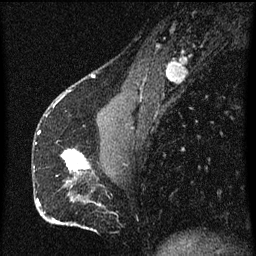
Breast MRI (dynamic contrast-enhanced), one sagittal slice; position 24 of 60 along the scan axis; dynamic contrast-enhanced series, image 2 of 3 at this slice position (ordered by acquisition); 1.5 T; TE 4.2 ms, TR 8 ms; 2 mm slice thickness; 256 × 256 image matrix, field of view 180 × 180 mm. Patient: female, 51 years.
Structures marked on this image (semi-automatically segmented with operator editing):
- analysis volume of interest (the breast-tissue region the enhancement analysis was run in; not a lesion): bounding box [x1, y1, x2, y2] px = [62, 150, 91, 175]
- tumour enhancement mask (voxels above the 70 % enhancement threshold inside the analysis volume of interest): [62, 150, 89, 173]